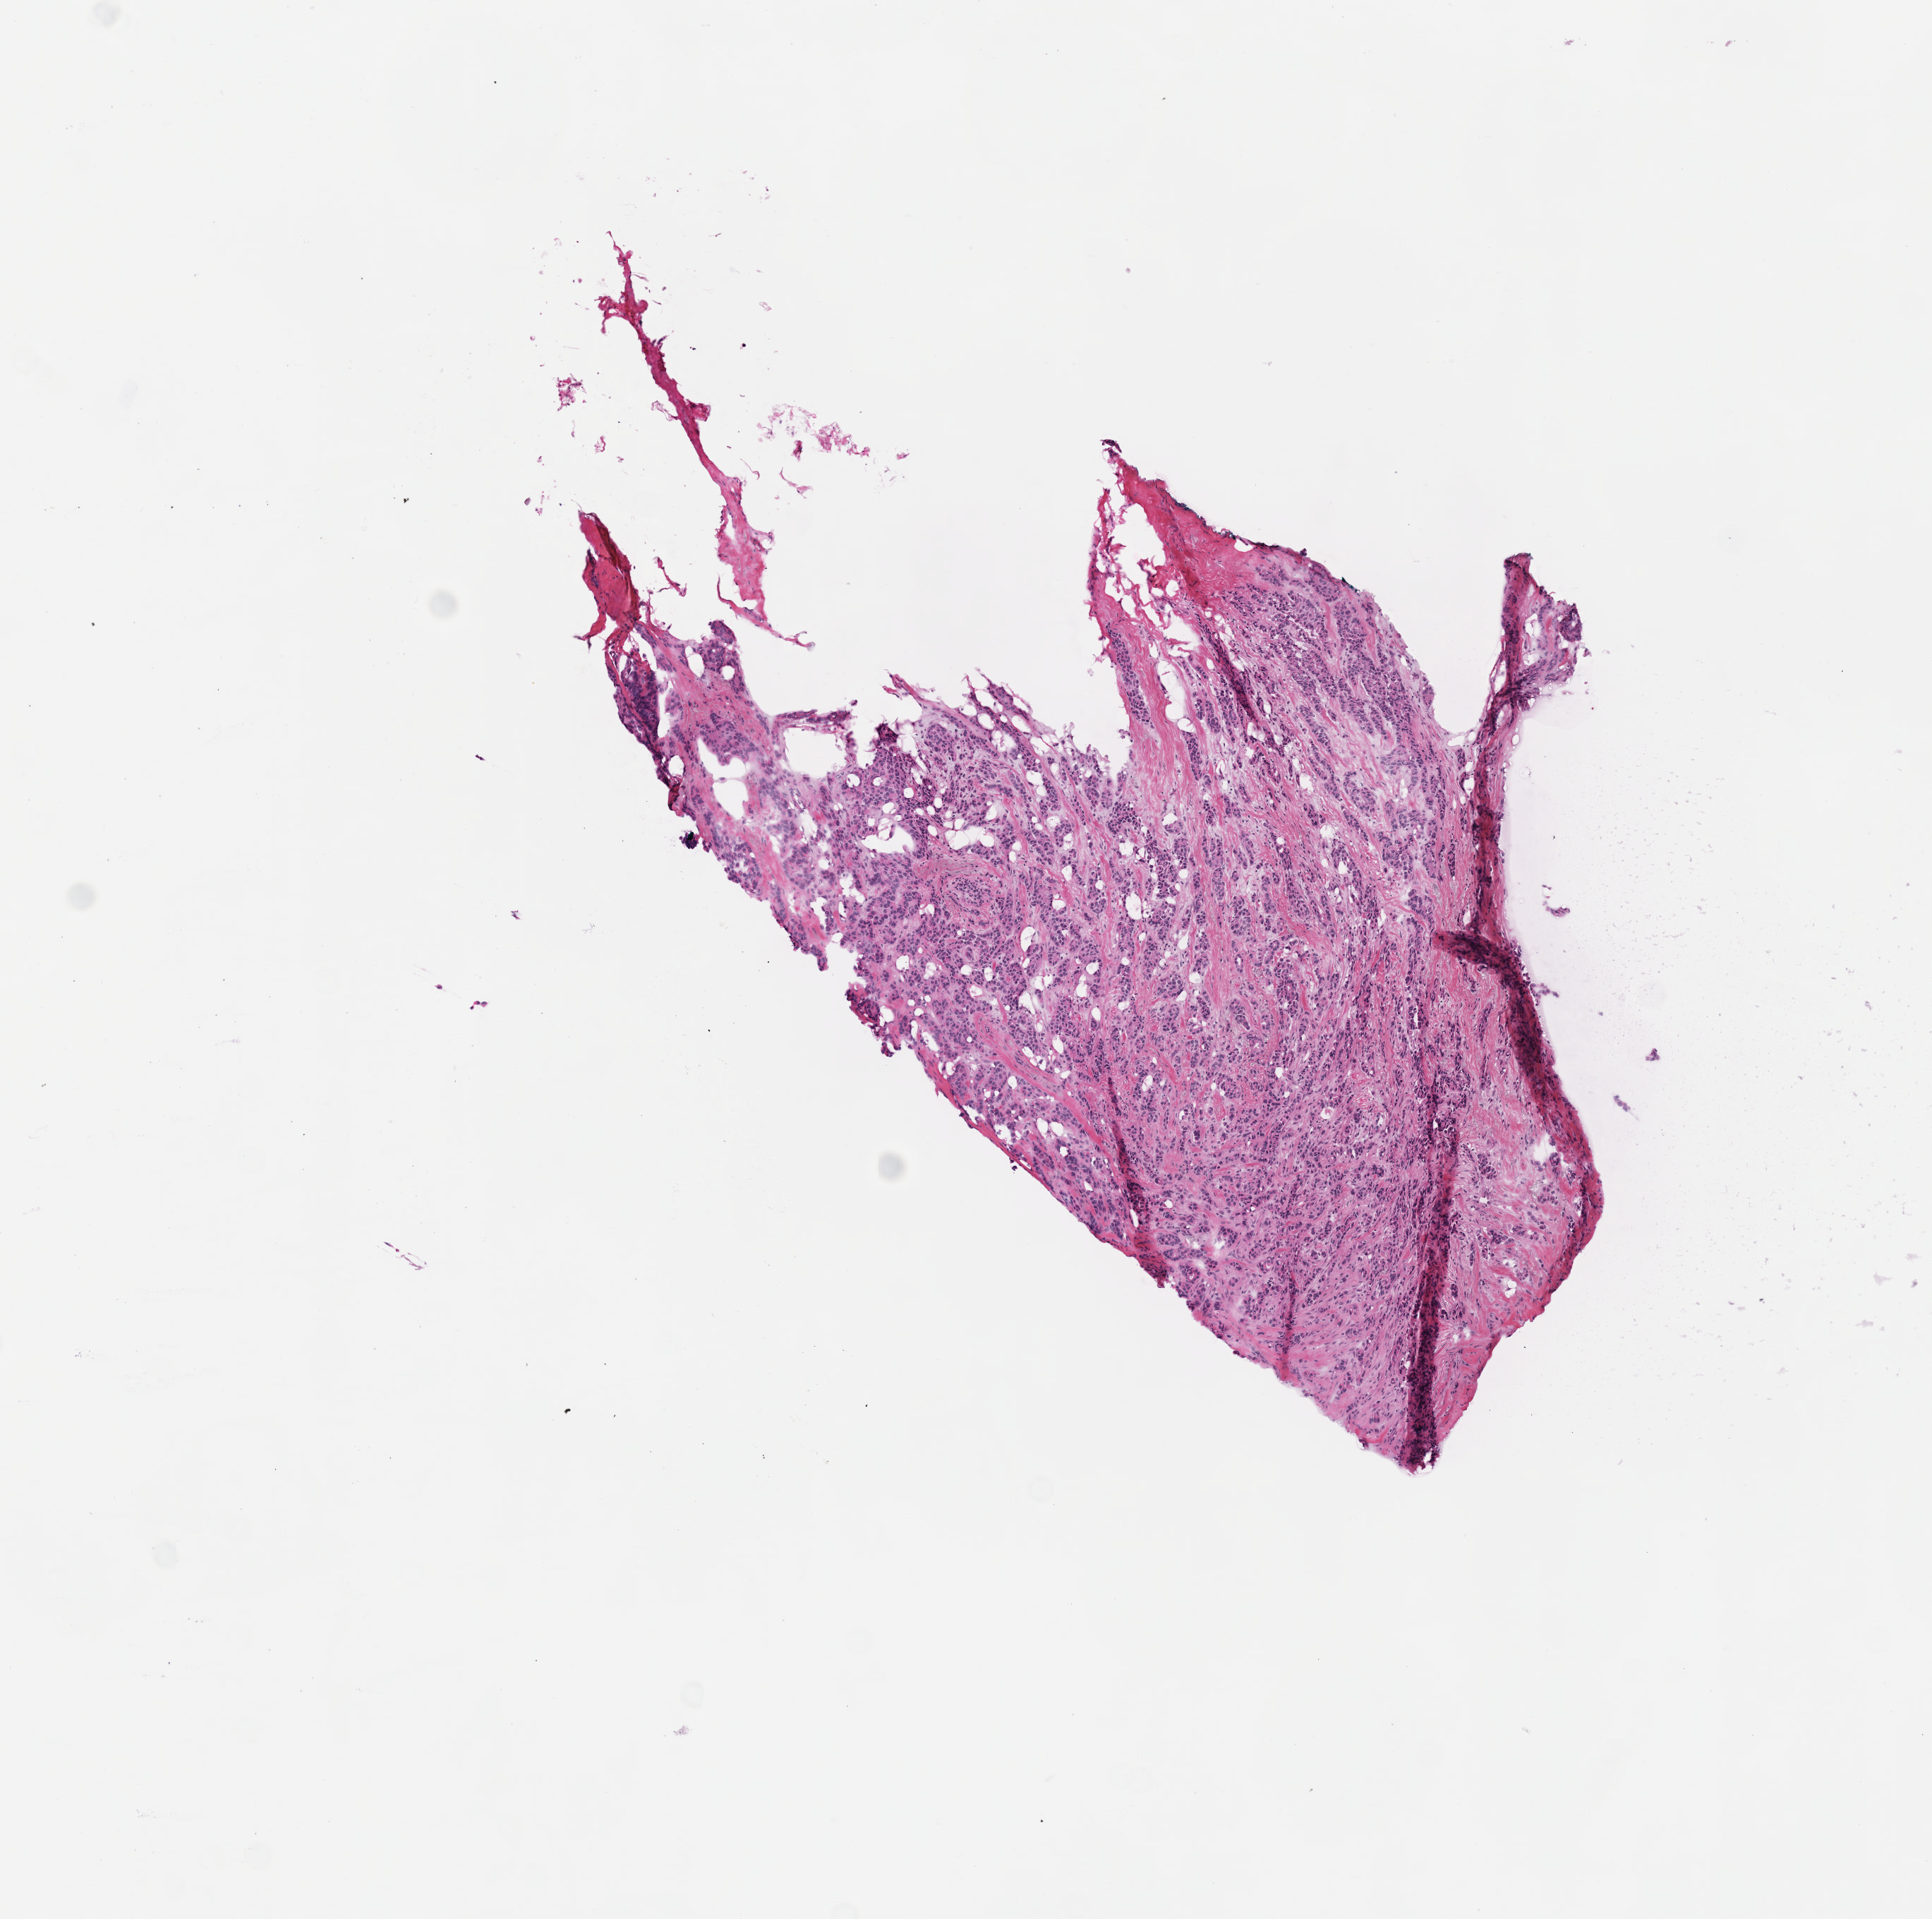
Digitized Hematoxylin and eosin (H&E) stained tissue section (whole slide), whole scanned area (about 5.5 x 5.5 mm, acquisition: 40x scan) shown as a low-resolution overview; frozen section from the top of the tissue portion; primary tumour sample from the breast. Patient: female, age at initial diagnosis 77 years. Slide review estimates, as recorded: tumour cells 100%, tumour nuclei 65%, normal cells 0%, stromal cells 0%, necrosis 0%. Inflammatory infiltration, as recorded: lymphocyte infiltration 2%, monocyte infiltration 0%, neutrophil infiltration 0%.
- TNM: T1c N0 (i-) MX
- diagnosis: Lobular carcinoma, NOS
- AJCC pathologic stage: IA (7th edition)